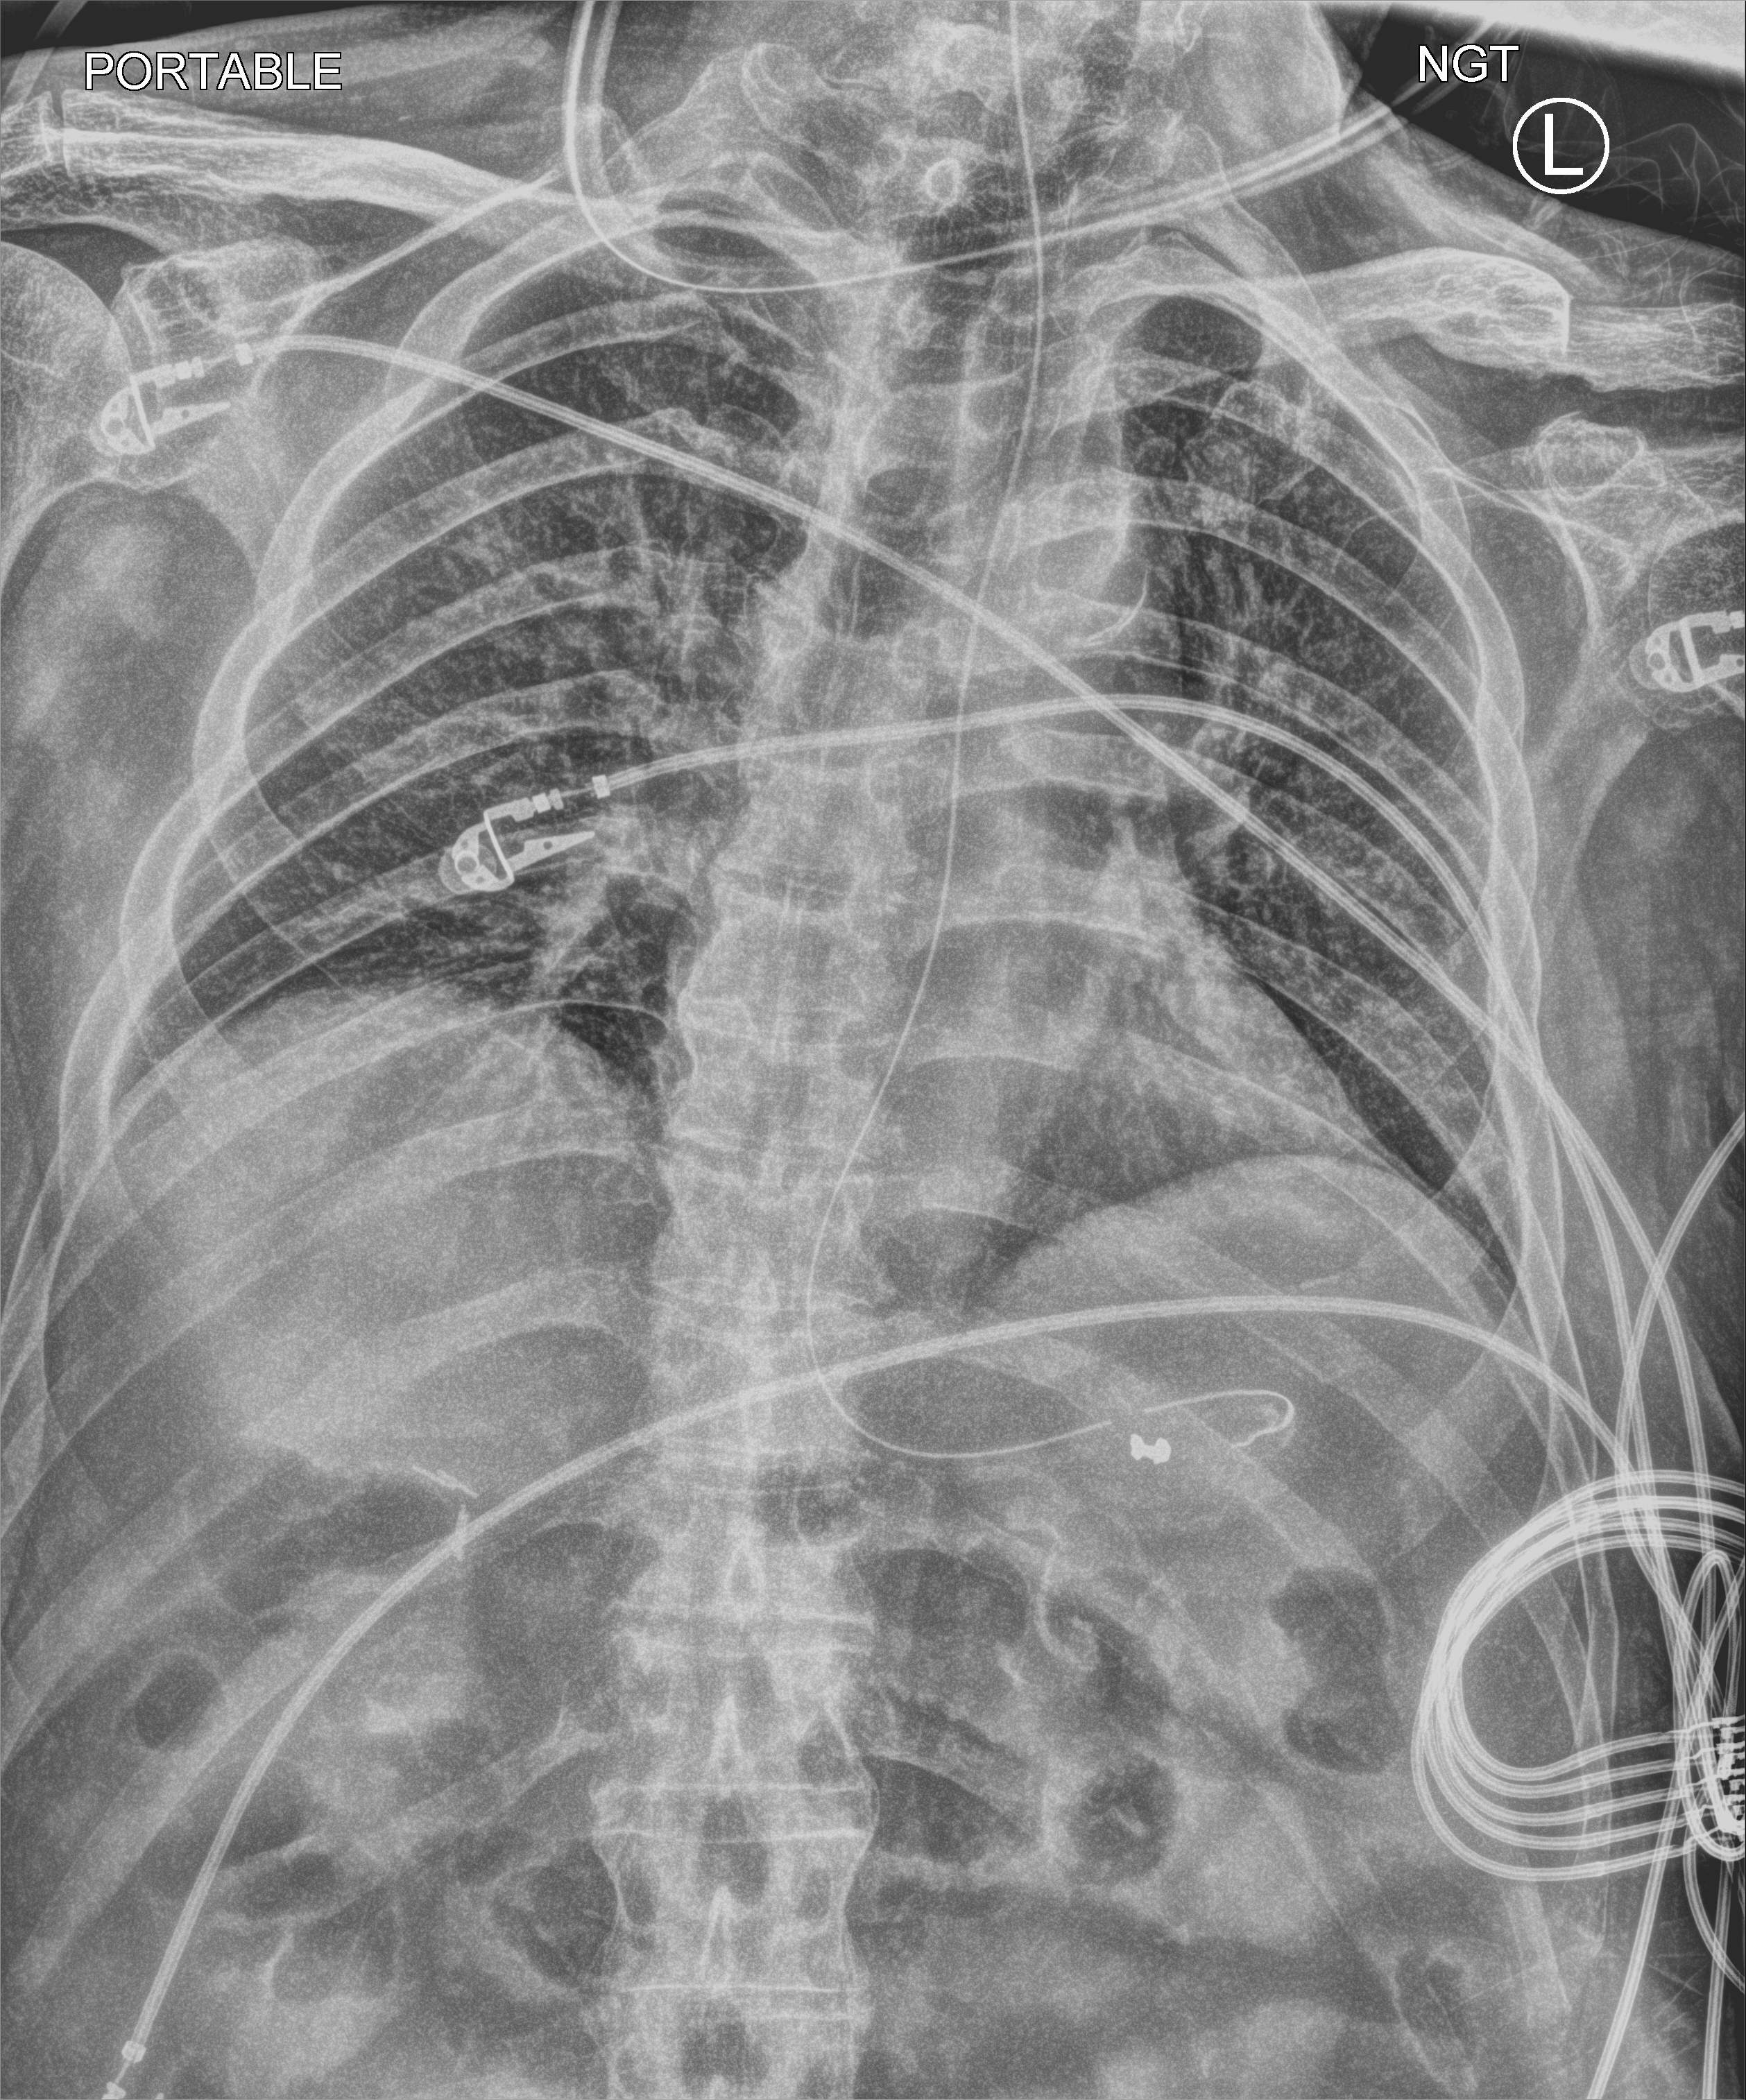
Chest X-ray (portable); anteroposterior (AP) projection. Patient hospitalised with COVID-19; male, aged 60–74 years.
Hospital-stay facts (about this admission, not read from this image; timing relative to this image not recorded): admitted to intensive care during this hospital stay: no; length of hospital stay: 5 days; mechanically ventilated during this hospital stay: no.